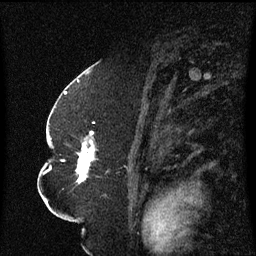
Breast MRI (dynamic contrast-enhanced), one sagittal slice. Position 38 of 60 along the scan axis. Dynamic contrast-enhanced series, image 2 of 3 at this slice position (ordered by acquisition). 1.5 T. TE 4.2 ms, TR 8.4 ms. 2.3 mm slice thickness. 256 × 256 image matrix, field of view 200 × 200 mm. Female patient, age 52 years. Case-level facts recorded for this patient, not image findings: setting: breast cancer imaged before/during neoadjuvant chemotherapy; receptor status: HR-positive, HER2-negative.
Outlined on this slice (semi-automatic segmentation, software-assisted and operator-edited):
- analysis volume of interest (the breast-tissue region the enhancement analysis was run in; not a lesion): bounding box <49,124,109,197> (left, top, right, bottom; pixels)
- tumour enhancement mask (voxels above the 70 % enhancement threshold inside the analysis volume of interest): <76,132,95,183>